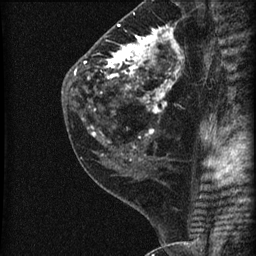
Breast MRI (dynamic contrast-enhanced), one sagittal slice; slice 28 of 60 in the series (ordered by position); dynamic contrast-enhanced series, image 2 of 3 at this slice position (ordered by acquisition); 1.5 T; TE 4.2 ms, TR 22.7 ms; 1.8 mm slice thickness; 256 × 256 image matrix, field of view 180 × 180 mm. Female patient, age 45 years. From the clinical record (not read from this slice): setting: breast cancer imaged before/during neoadjuvant chemotherapy; receptor status: HR-positive, HER2-negative.
Structures marked on this image (semi-automatic segmentation, software-assisted and operator-edited):
- analysis volume of interest (the breast-tissue region the enhancement analysis was run in; not a lesion): bounding box [x1, y1, x2, y2] px = [74, 11, 205, 140]
- tumour enhancement mask (voxels above the 90 % enhancement threshold inside the analysis volume of interest): [75, 25, 181, 136]